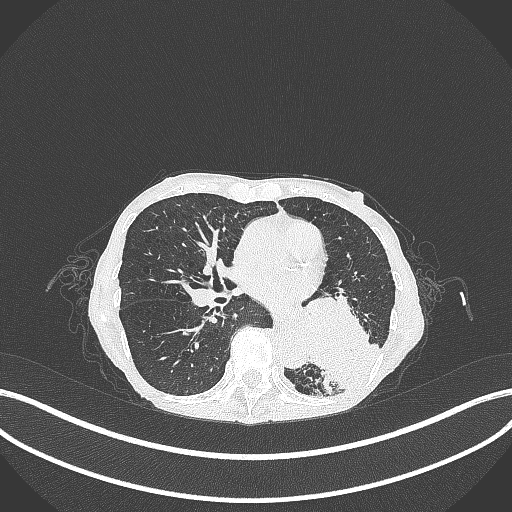
Chest CT, one axial slice; slice 129 of 347 in the series (ordered by position); reconstruction kernel B70f; 120 kVp; lung window (W 1500 / L -600 HU); 1 mm slice thickness; 512 × 512 image matrix, field of view 400 × 400 mm. Patient: female, 70 years. Case-level facts recorded for this patient, not image findings: clinical TNM (as recorded): T3 N0 M0.
Outlined on this slice (rectangle marked by the reading radiologist):
- lung tumour (recorded histology: small cell carcinoma): box from (x=298, y=289) to (x=385, y=396) px